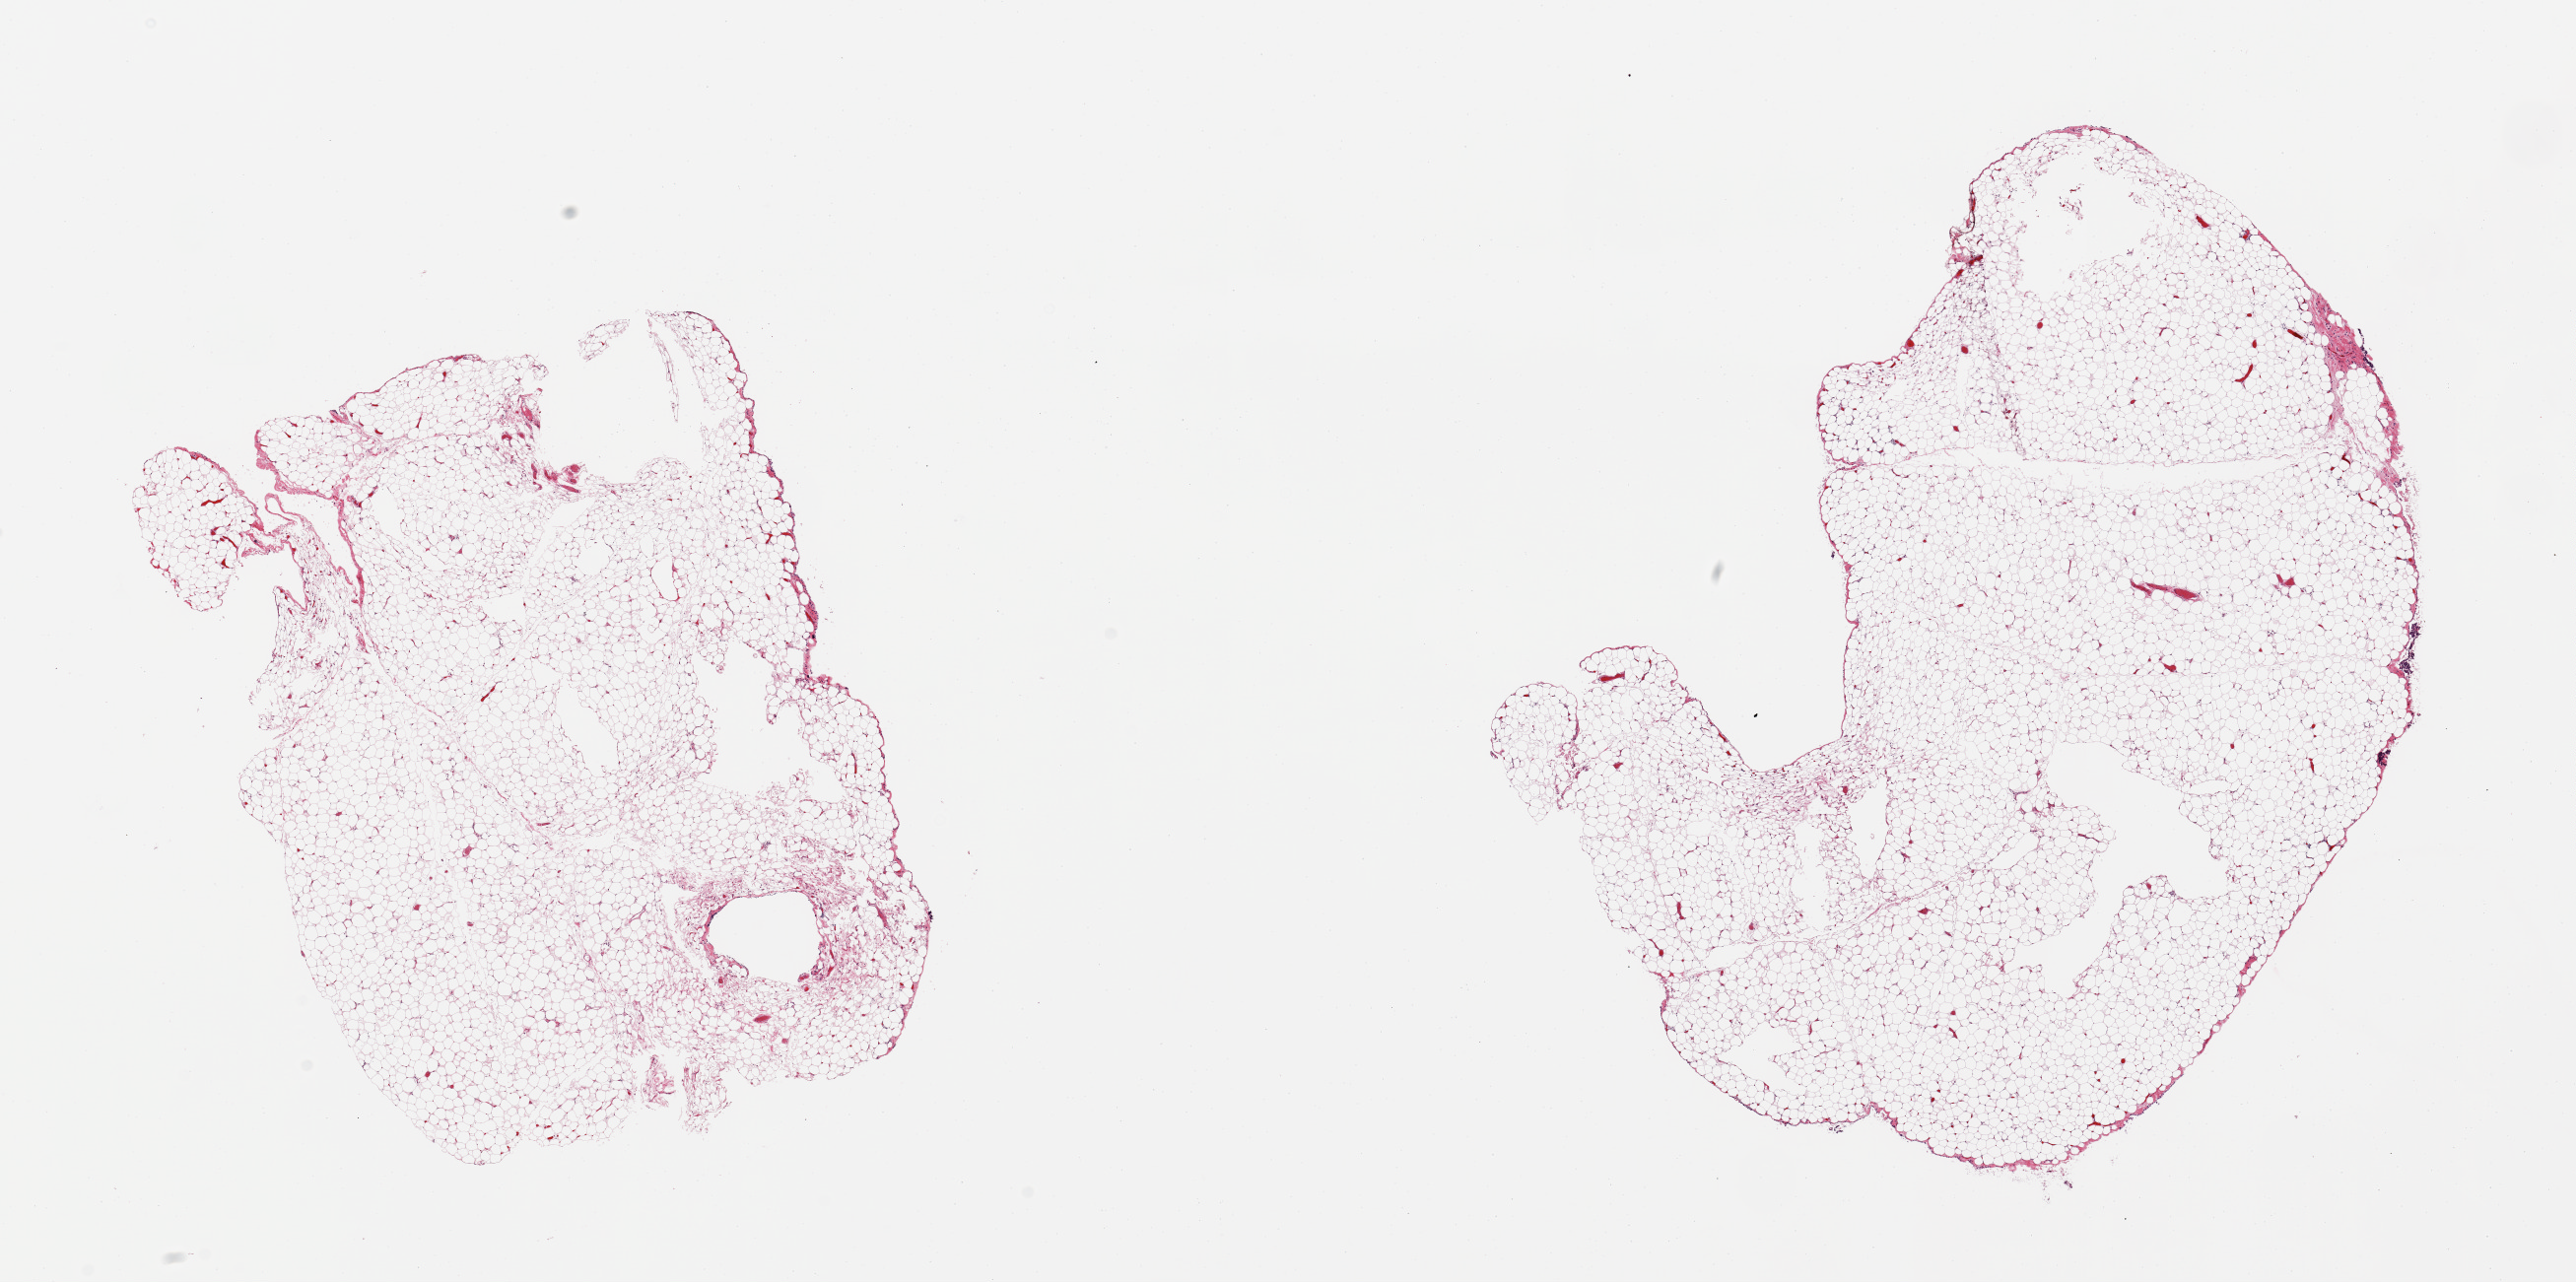
Hematoxylin and eosin (H&E) whole-slide image — low-resolution overview of the scanned area, about 20.7 x 10.3 mm (acquisition: 20x scan), PAXgene-fixed paraffin-embedded (PFPE) section, section of omentum (target tissue), donor tissue sample. Female donor.
Pathologist's review note for this sample: 2 pieces; no fibrous content.